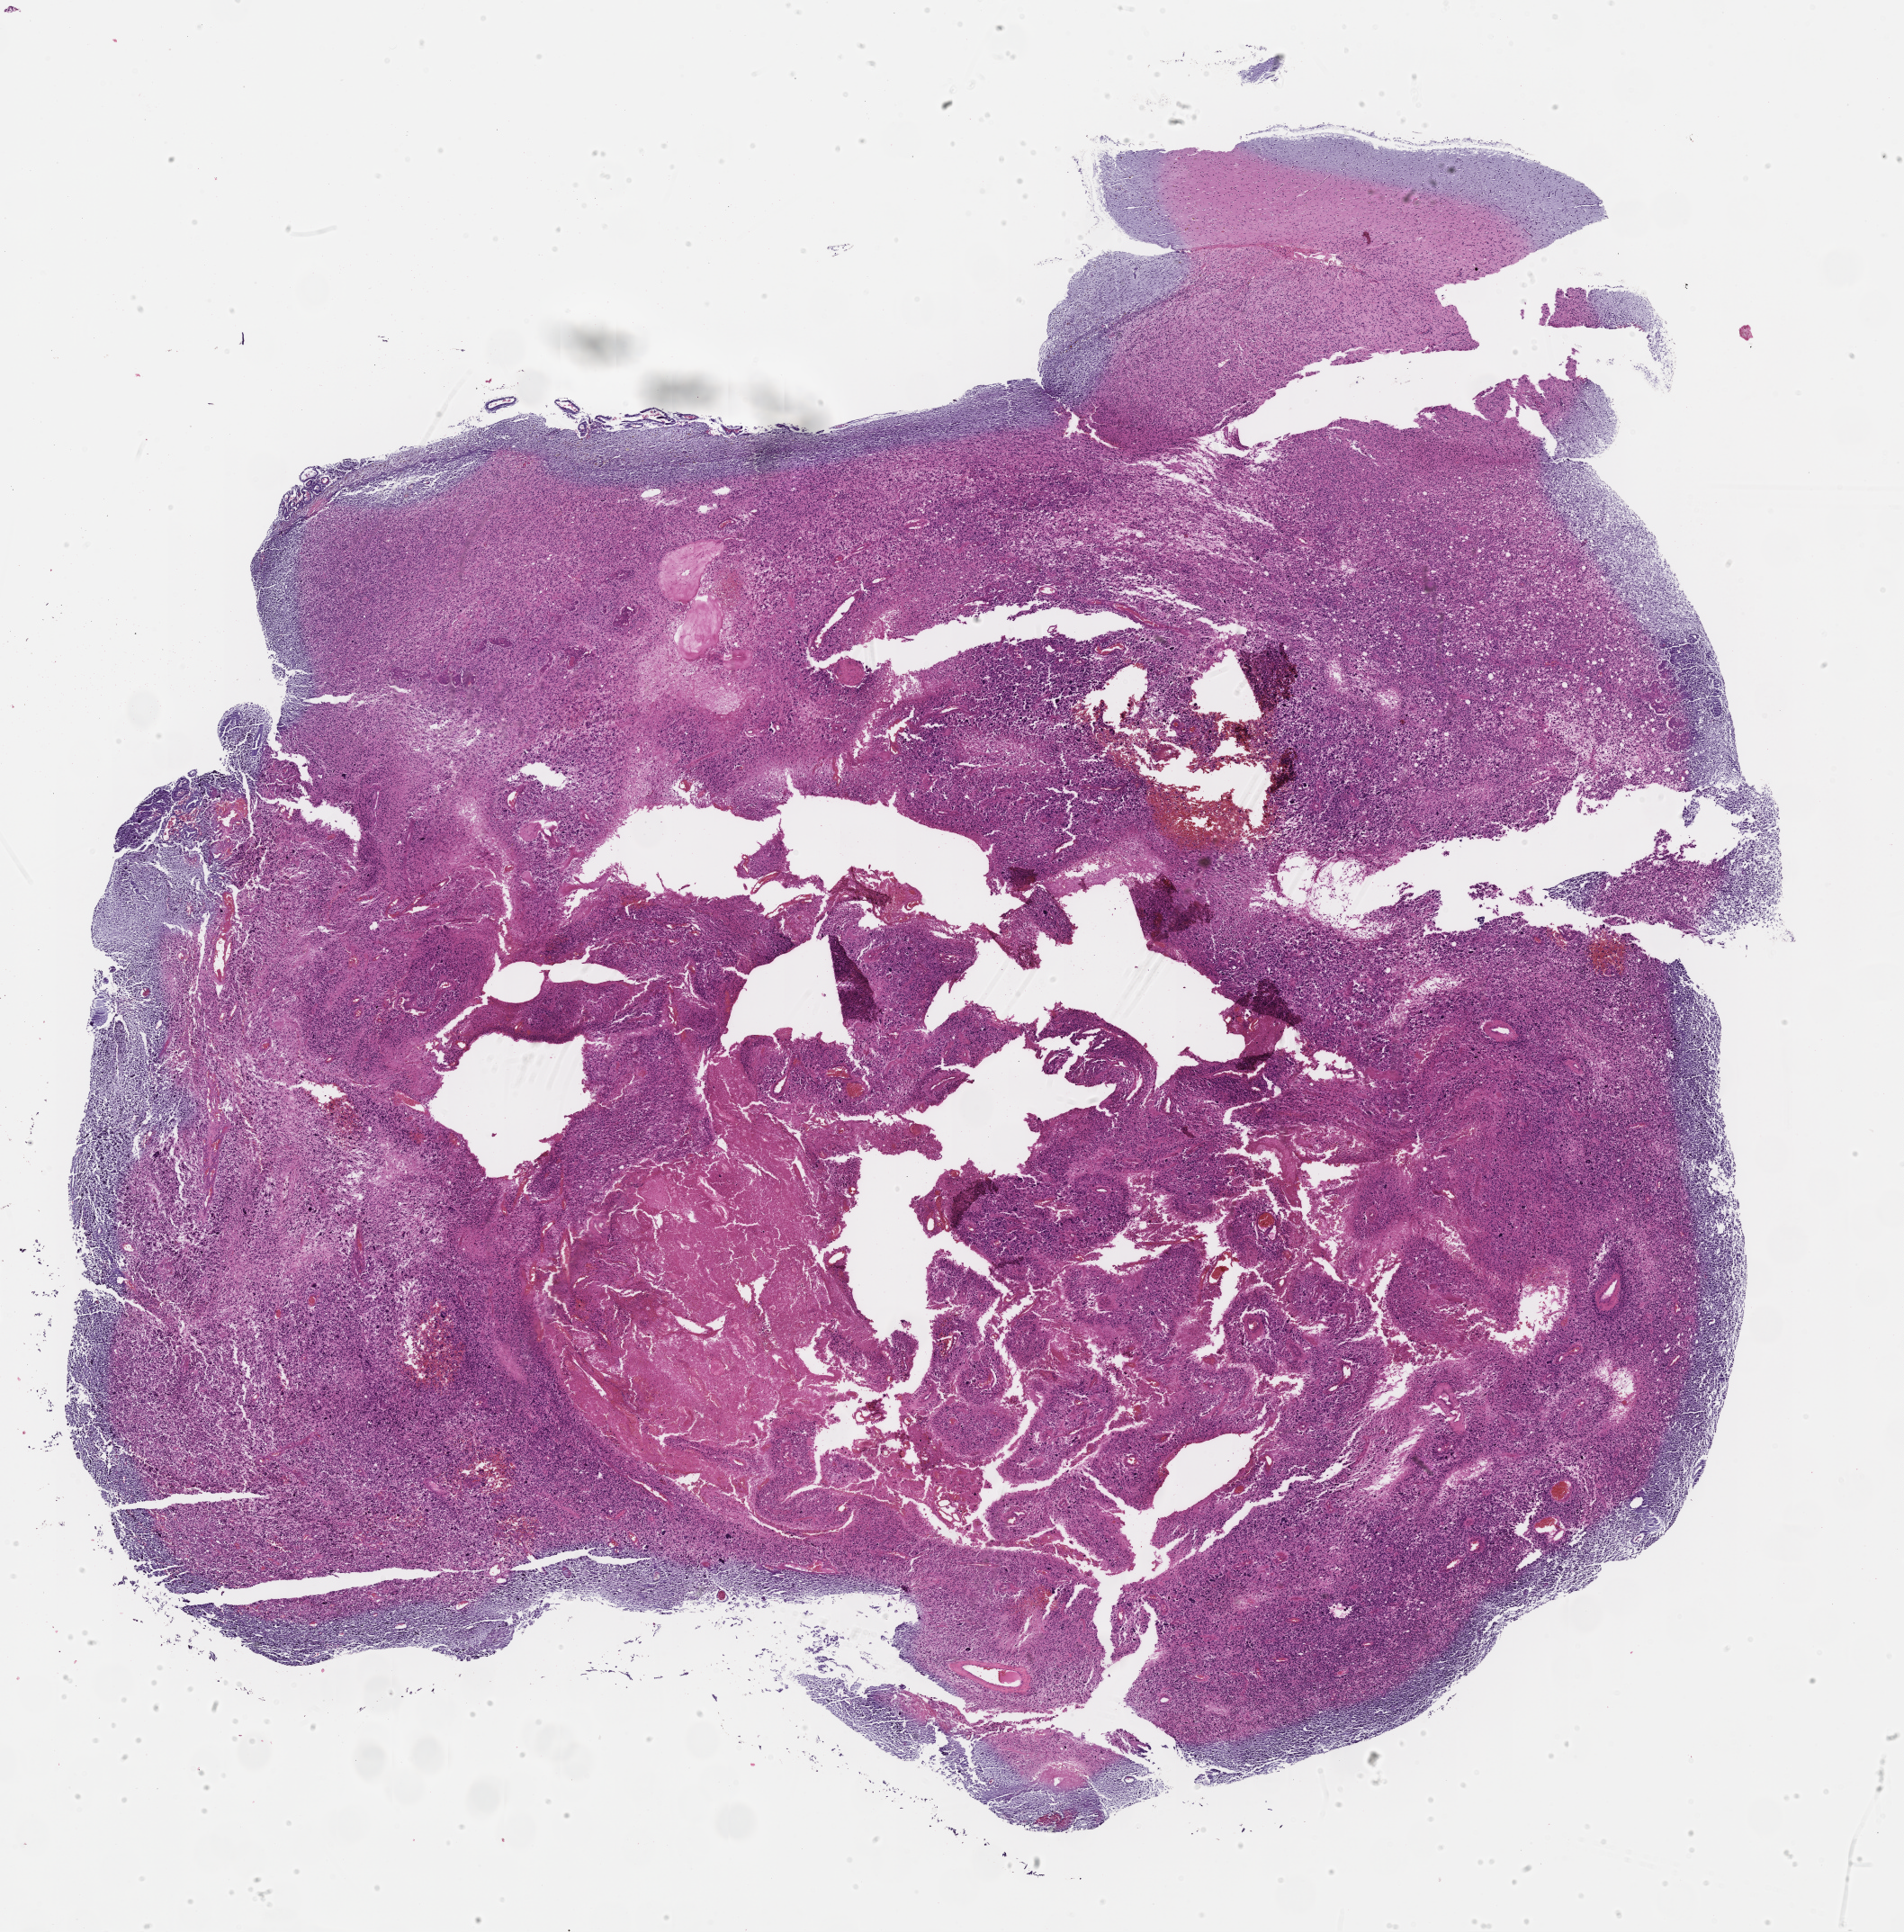
Digitized H&E tissue section (whole slide) — whole scanned area (about 17.2 x 17.4 mm) shown as a low-resolution overview; formalin-fixed paraffin-embedded (FFPE) diagnostic section; sample: primary tumour, brain. Female patient; age at initial diagnosis 36 years.
- histologic diagnosis: Glioblastoma